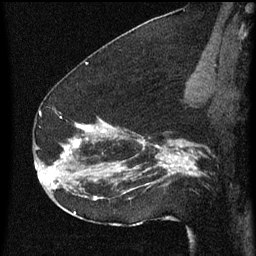
Breast MRI (dynamic contrast-enhanced), one sagittal slice. Position 37 of 60 along the scan axis. Dynamic contrast-enhanced series, image 2 of 3 at this slice position (ordered by acquisition). 1.5 T. TE 4.2 ms, TR 8 ms. 2 mm slice thickness. 256 × 256 image matrix, field of view 180 × 180 mm. Female patient, age 52 years.
Outlined on this slice (semi-automatically segmented with operator editing):
- analysis volume of interest (the breast-tissue region the enhancement analysis was run in; not a lesion): bounding box <54,110,178,207> (left, top, right, bottom; pixels)
- tumour enhancement mask (voxels above the 70 % enhancement threshold inside the analysis volume of interest): <60,124,178,201>